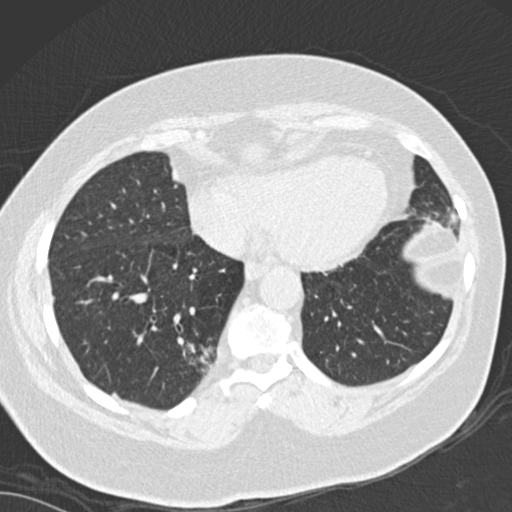
Low-dose screening chest CT, axial slice. Baseline annual screen. Lung window (W 1500 / L -600 HU). 2 mm slice thickness. 120 kVp. Slice 113 of 162 in the series. 512 × 512 image matrix. Female, age 66 years at enrolment. Current smoker at enrolment.
Lesion marked by an expert reader, bounding box (x1, y1, x2, y2) in pixels: (141, 310, 239, 412). The screening reader recorded 3 non-calcified nodules or masses ≥4 mm on this exam (left lower lobe, left lower lobe, right lower lobe); which of them this box marks is not recorded. Official screen result: positive, change unspecified: nodule(s) >= 4 mm or enlarging nodule(s), mass(es), or other non-specific abnormalities suspicious for lung cancer. Lung cancer was diagnosed 67 days after this screen: adenocarcinoma, NOS, right lower lobe, well differentiated (G1), stage IB (AJCC 6th edition), 55 mm at pathology.